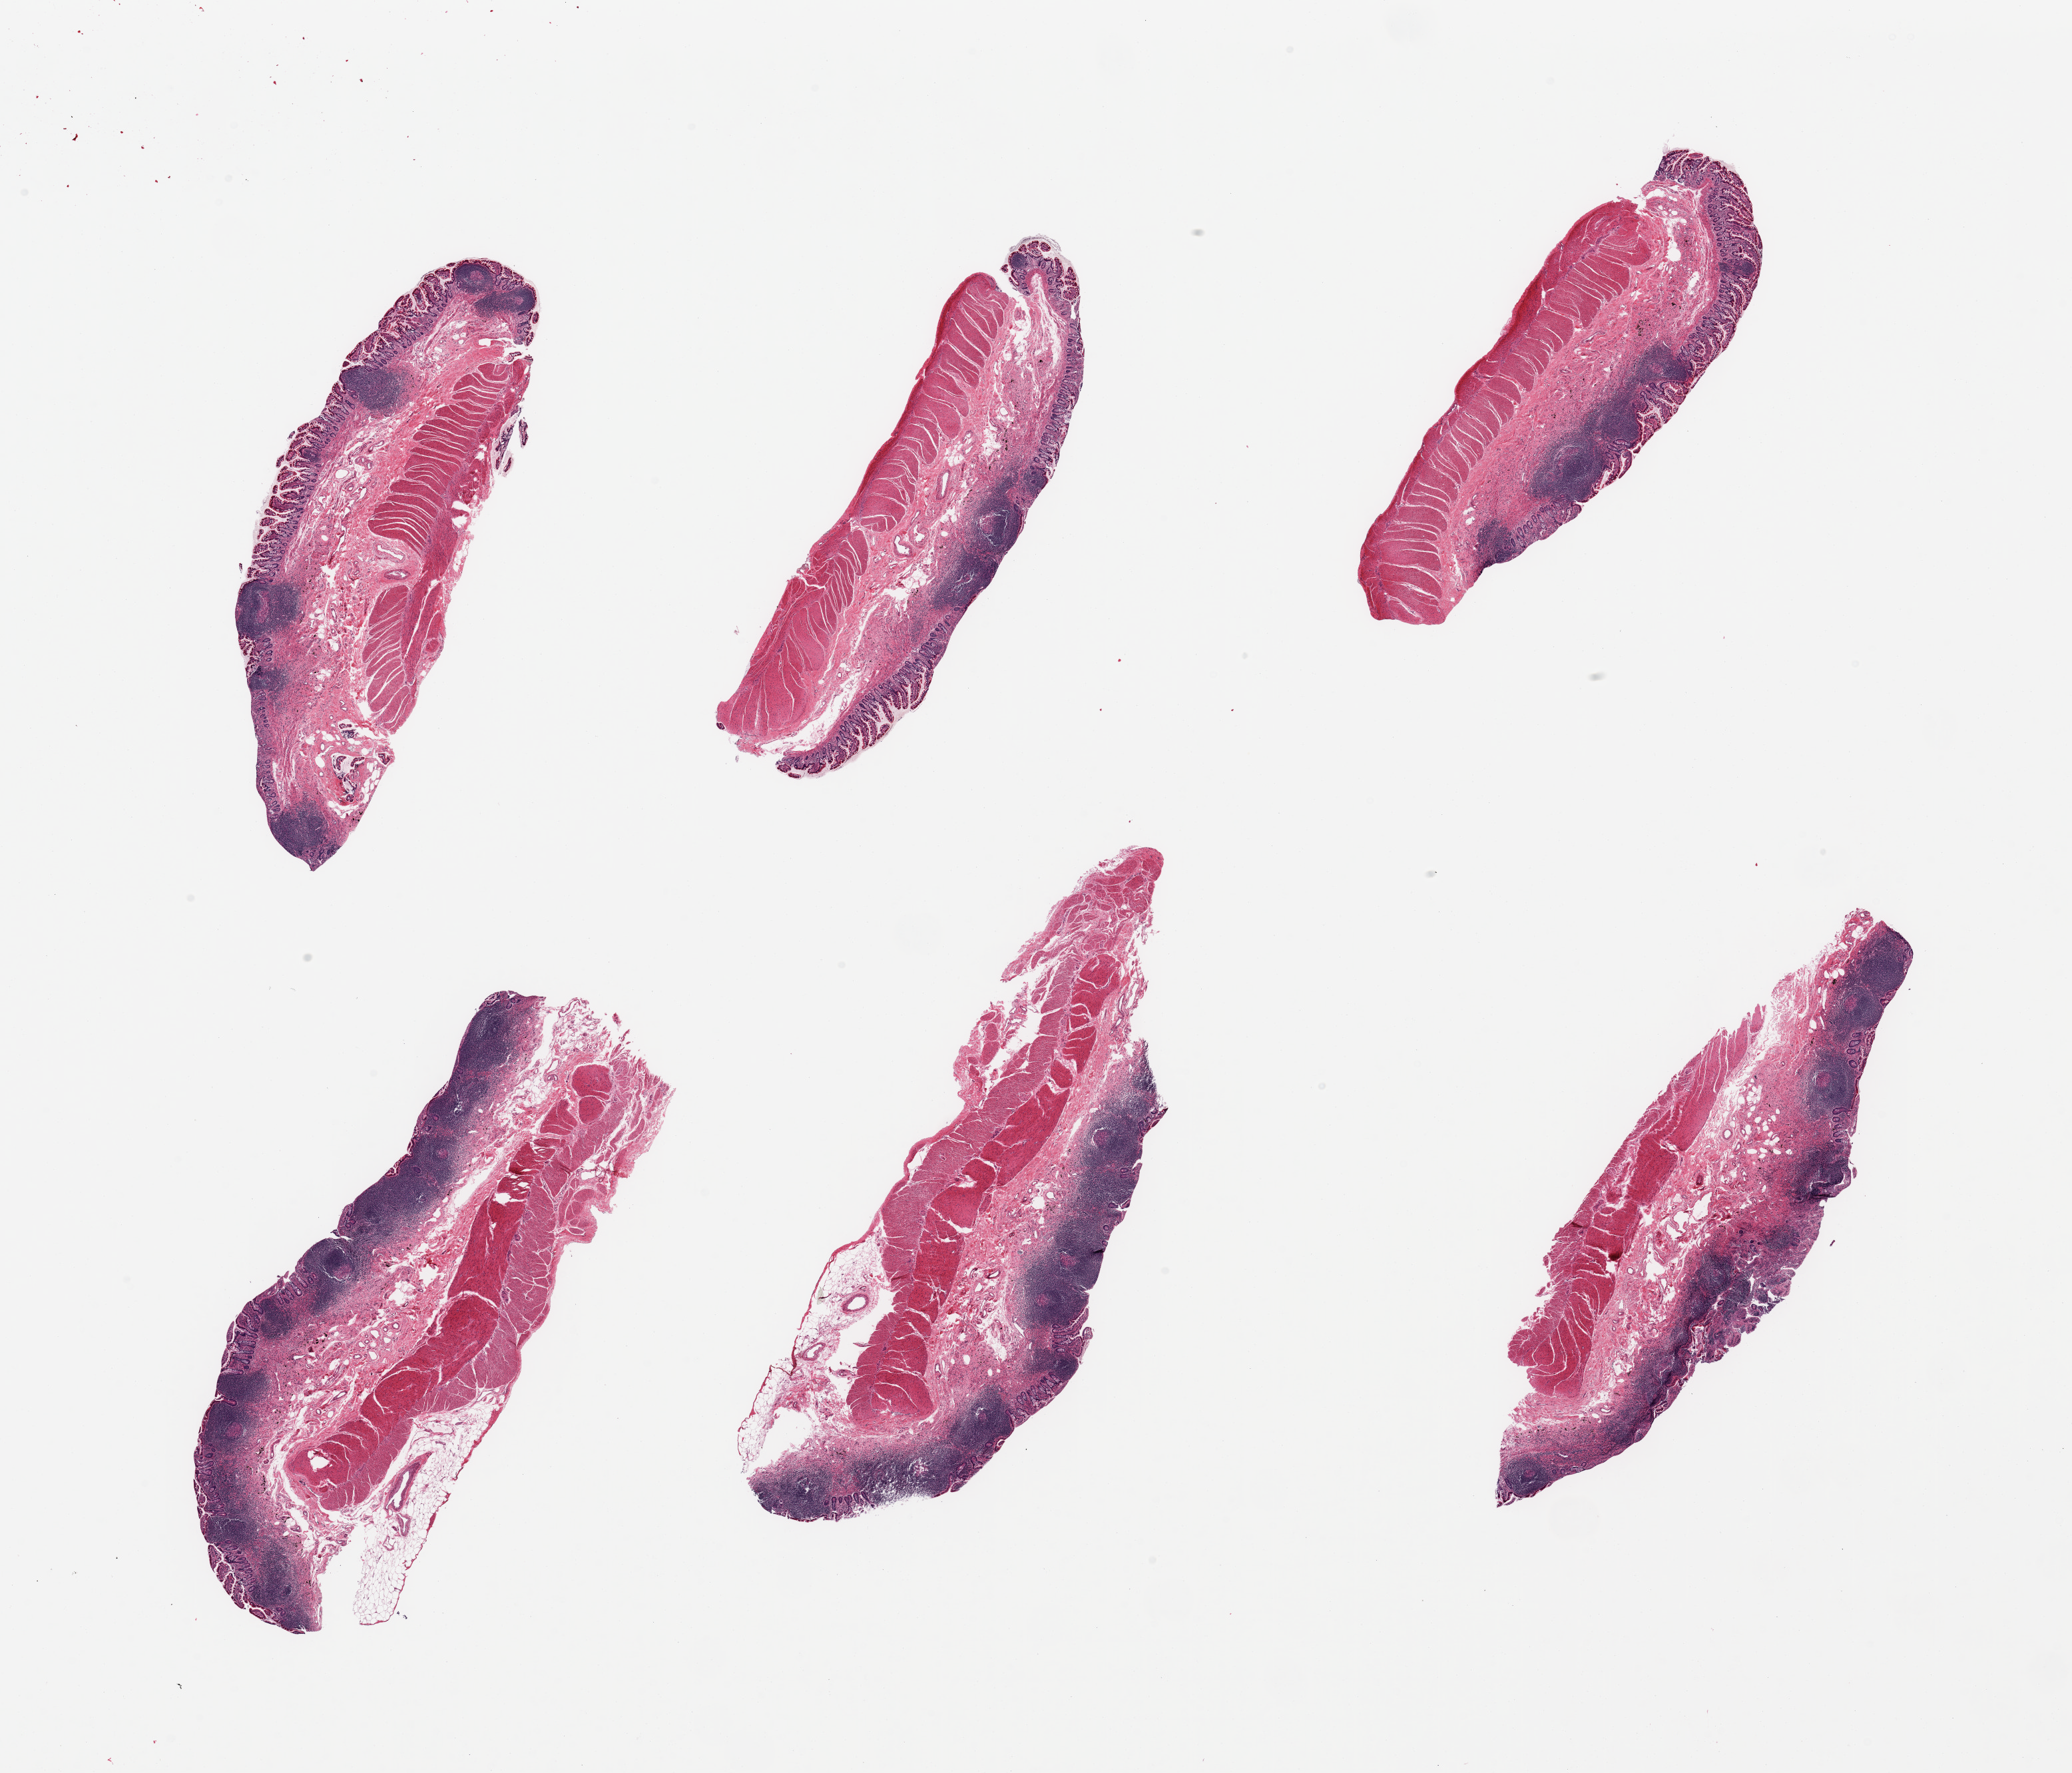
Hematoxylin and eosin (H&E) whole-slide image — shown as a low-resolution overview of the whole scanned area (about 24.6 x 21.1 mm, slide scanned at 20x). Donor sex: female.
Specimen: PAXgene-fixed paraffin-embedded (PFPE) section; section of ileum (target tissue); donor tissue sample.